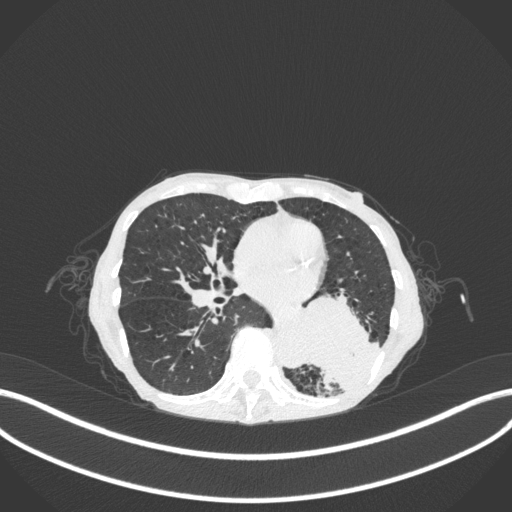
Chest CT, one axial slice; slice 127 of 347 in the series (ordered by position); 120 kVp; lung window (W 1500 / L -600 HU); 512 × 512 image matrix. Patient: female, 70 years. From the clinical record (not read from this slice): clinical TNM (as recorded): T3 N0 M0; histopathological grade: G3.
Outlined on this slice (bounding box drawn by a radiologist):
- lung tumour (recorded histology: small cell carcinoma): box from (x=287, y=281) to (x=378, y=391) px